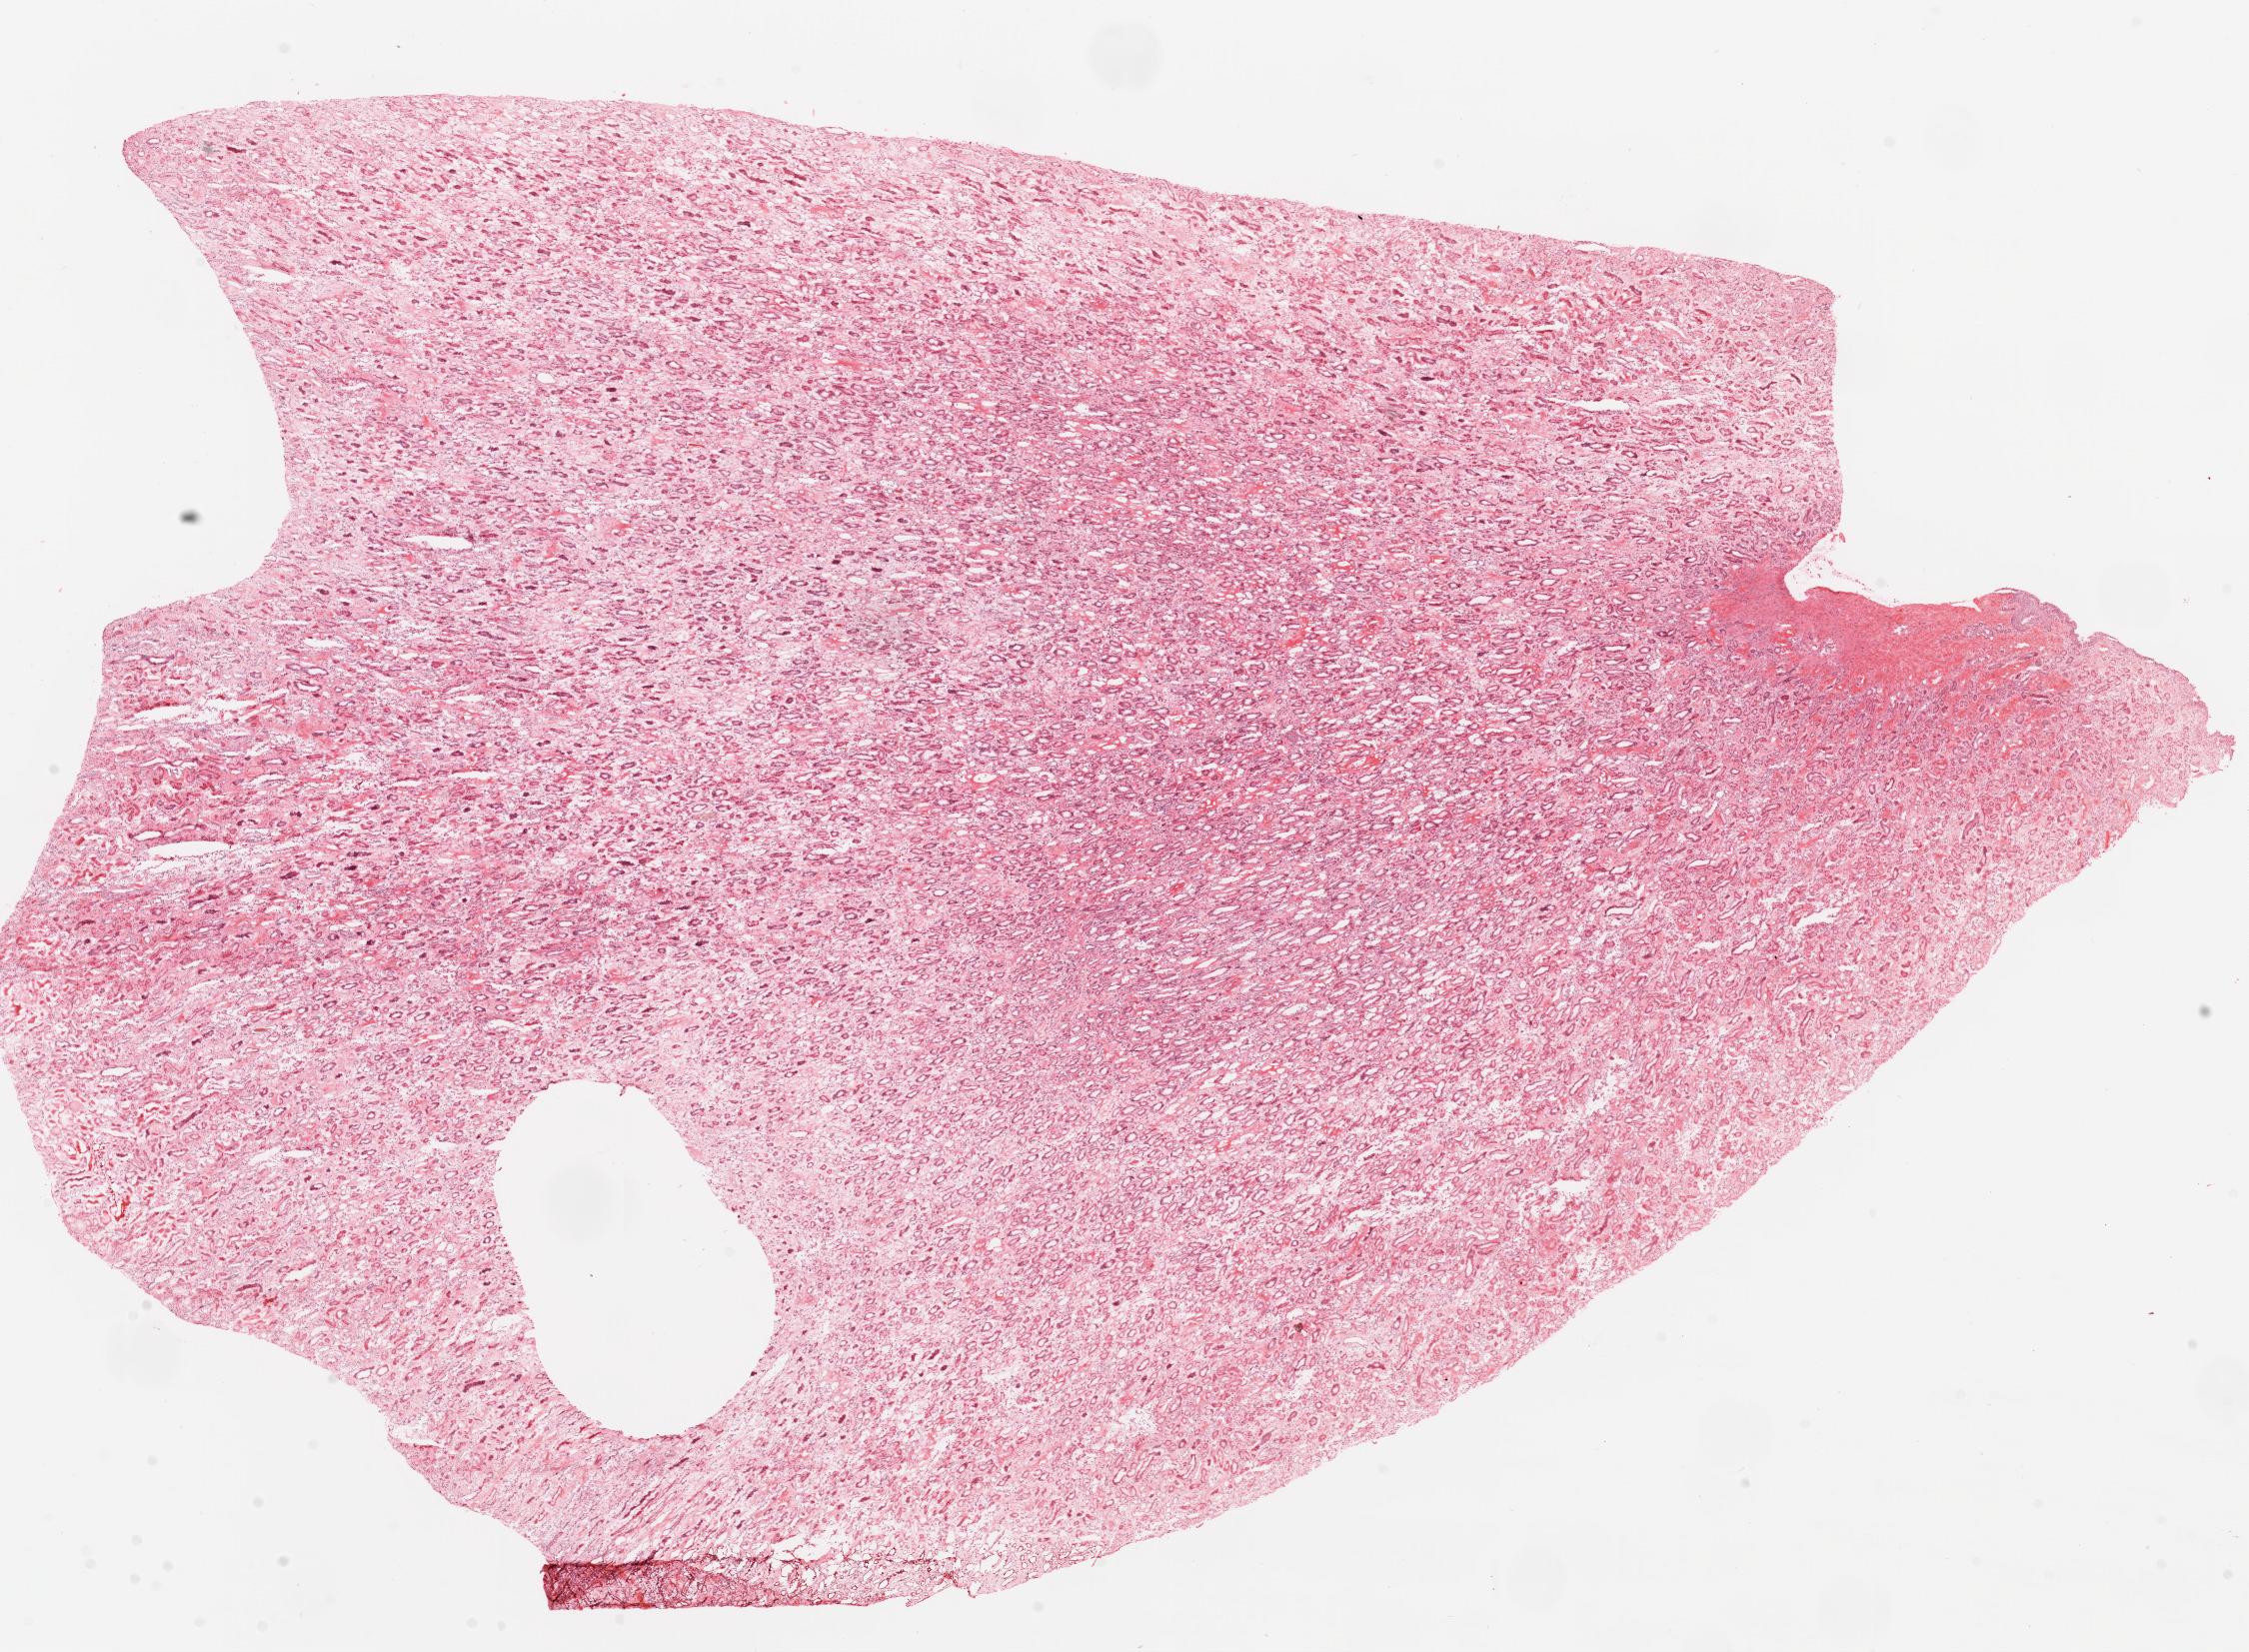
Whole-slide histology image, H&E, low-resolution overview of the scanned area, about 18.1 x 13.3 mm (slide scanned at 20x), frozen section from the top of the tissue portion, kidney, solid tissue normal (non-tumour tissue) sample. Patient: male, age at initial diagnosis 62 years.
- this section: solid tissue normal (non-tumour) sample from the same patient
- patient diagnosis: Clear cell adenocarcinoma, NOS